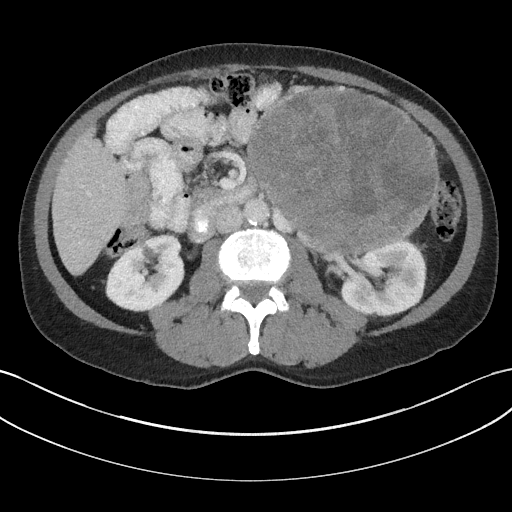
Contrast-enhanced abdominal CT, one axial slice. Slice 89 of 147 in the series (ordered by position). Reconstruction kernel I31f/3. 100 kVp. Soft-tissue window (W 400 / L 40 HU). 3 mm slice thickness. 512 × 512 image matrix, field of view 384 × 384 mm. Male patient, age 58 years. From the clinical record (not read from this slice): diagnosis: adrenocortical carcinoma; tumour side: left adrenal; tumour size at pathology: 22 cm; Ki-67 index: 26 %.
Annotated regions visible in this slice (semi-automatic segmentation, software-assisted and operator-edited):
- mass: box from (x=250, y=91) to (x=437, y=252) px